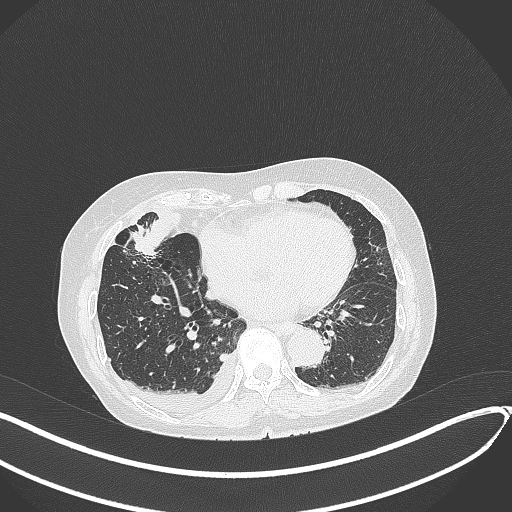
Chest CT, one axial slice. Slice 139 of 418 in the series (ordered by position). Lung window (W 1500 / L -600 HU). 512 × 512 image matrix. Female patient, age 75 years. Case-level facts recorded for this patient, not image findings: clinical TNM (as recorded): T2a N3 M0.
Outlined on this slice (rectangle marked by the reading radiologist):
- lung tumour (recorded histology: adenocarcinoma): bounding box <127,226,165,257> (left, top, right, bottom; pixels)